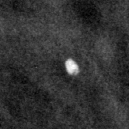
Region of interest cut from a scanned film mammogram (one marked finding); left breast; CC view.
- Marked abnormality: calcifications, morphology lucent centered; BI-RADS assessment category 2; benign without callback (not worked up further).